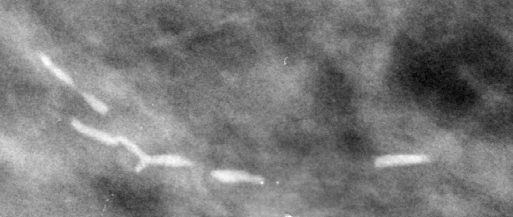
Cropped region of a digitized screen-film mammogram centred on a radiologist-marked abnormality, left breast, MLO view.
Finding: calcifications, morphology large rodlike / round and regular, distribution regional; BI-RADS assessment category 2; benign; no additional work-up was recommended (benign without callback).